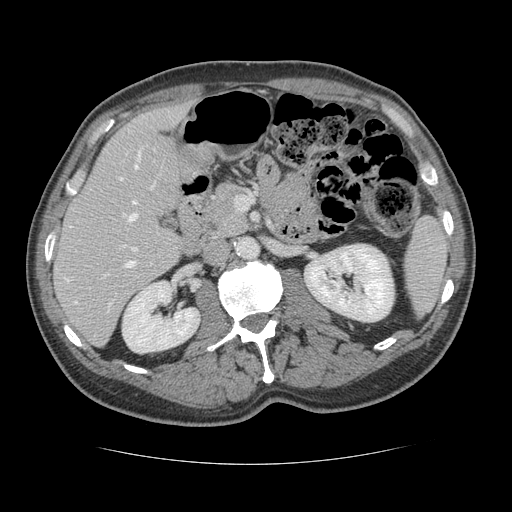
Contrast-enhanced abdominal CT, one axial slice; position 65 of 134 along the scan axis; reconstruction kernel STANDARD; 120 kVp; intravenous contrast given; soft-tissue window (W 400 / L 40 HU); 2.5 mm slice thickness; 512 × 512 image matrix. Male patient, age 68 years. Case-level facts recorded for this patient, not image findings: diagnosis: colorectal cancer liver metastases, imaged before liver resection.
Structures marked on this image (outlined manually by an expert reader):
- hepatic veins: bounding box <68,151,154,304> (left, top, right, bottom; pixels)
- liver: <55,107,187,344>
- planned liver remnant (the part of the liver to remain after resection): <55,106,187,335>
- portal vein (with intrahepatic branches): <123,213,136,267>